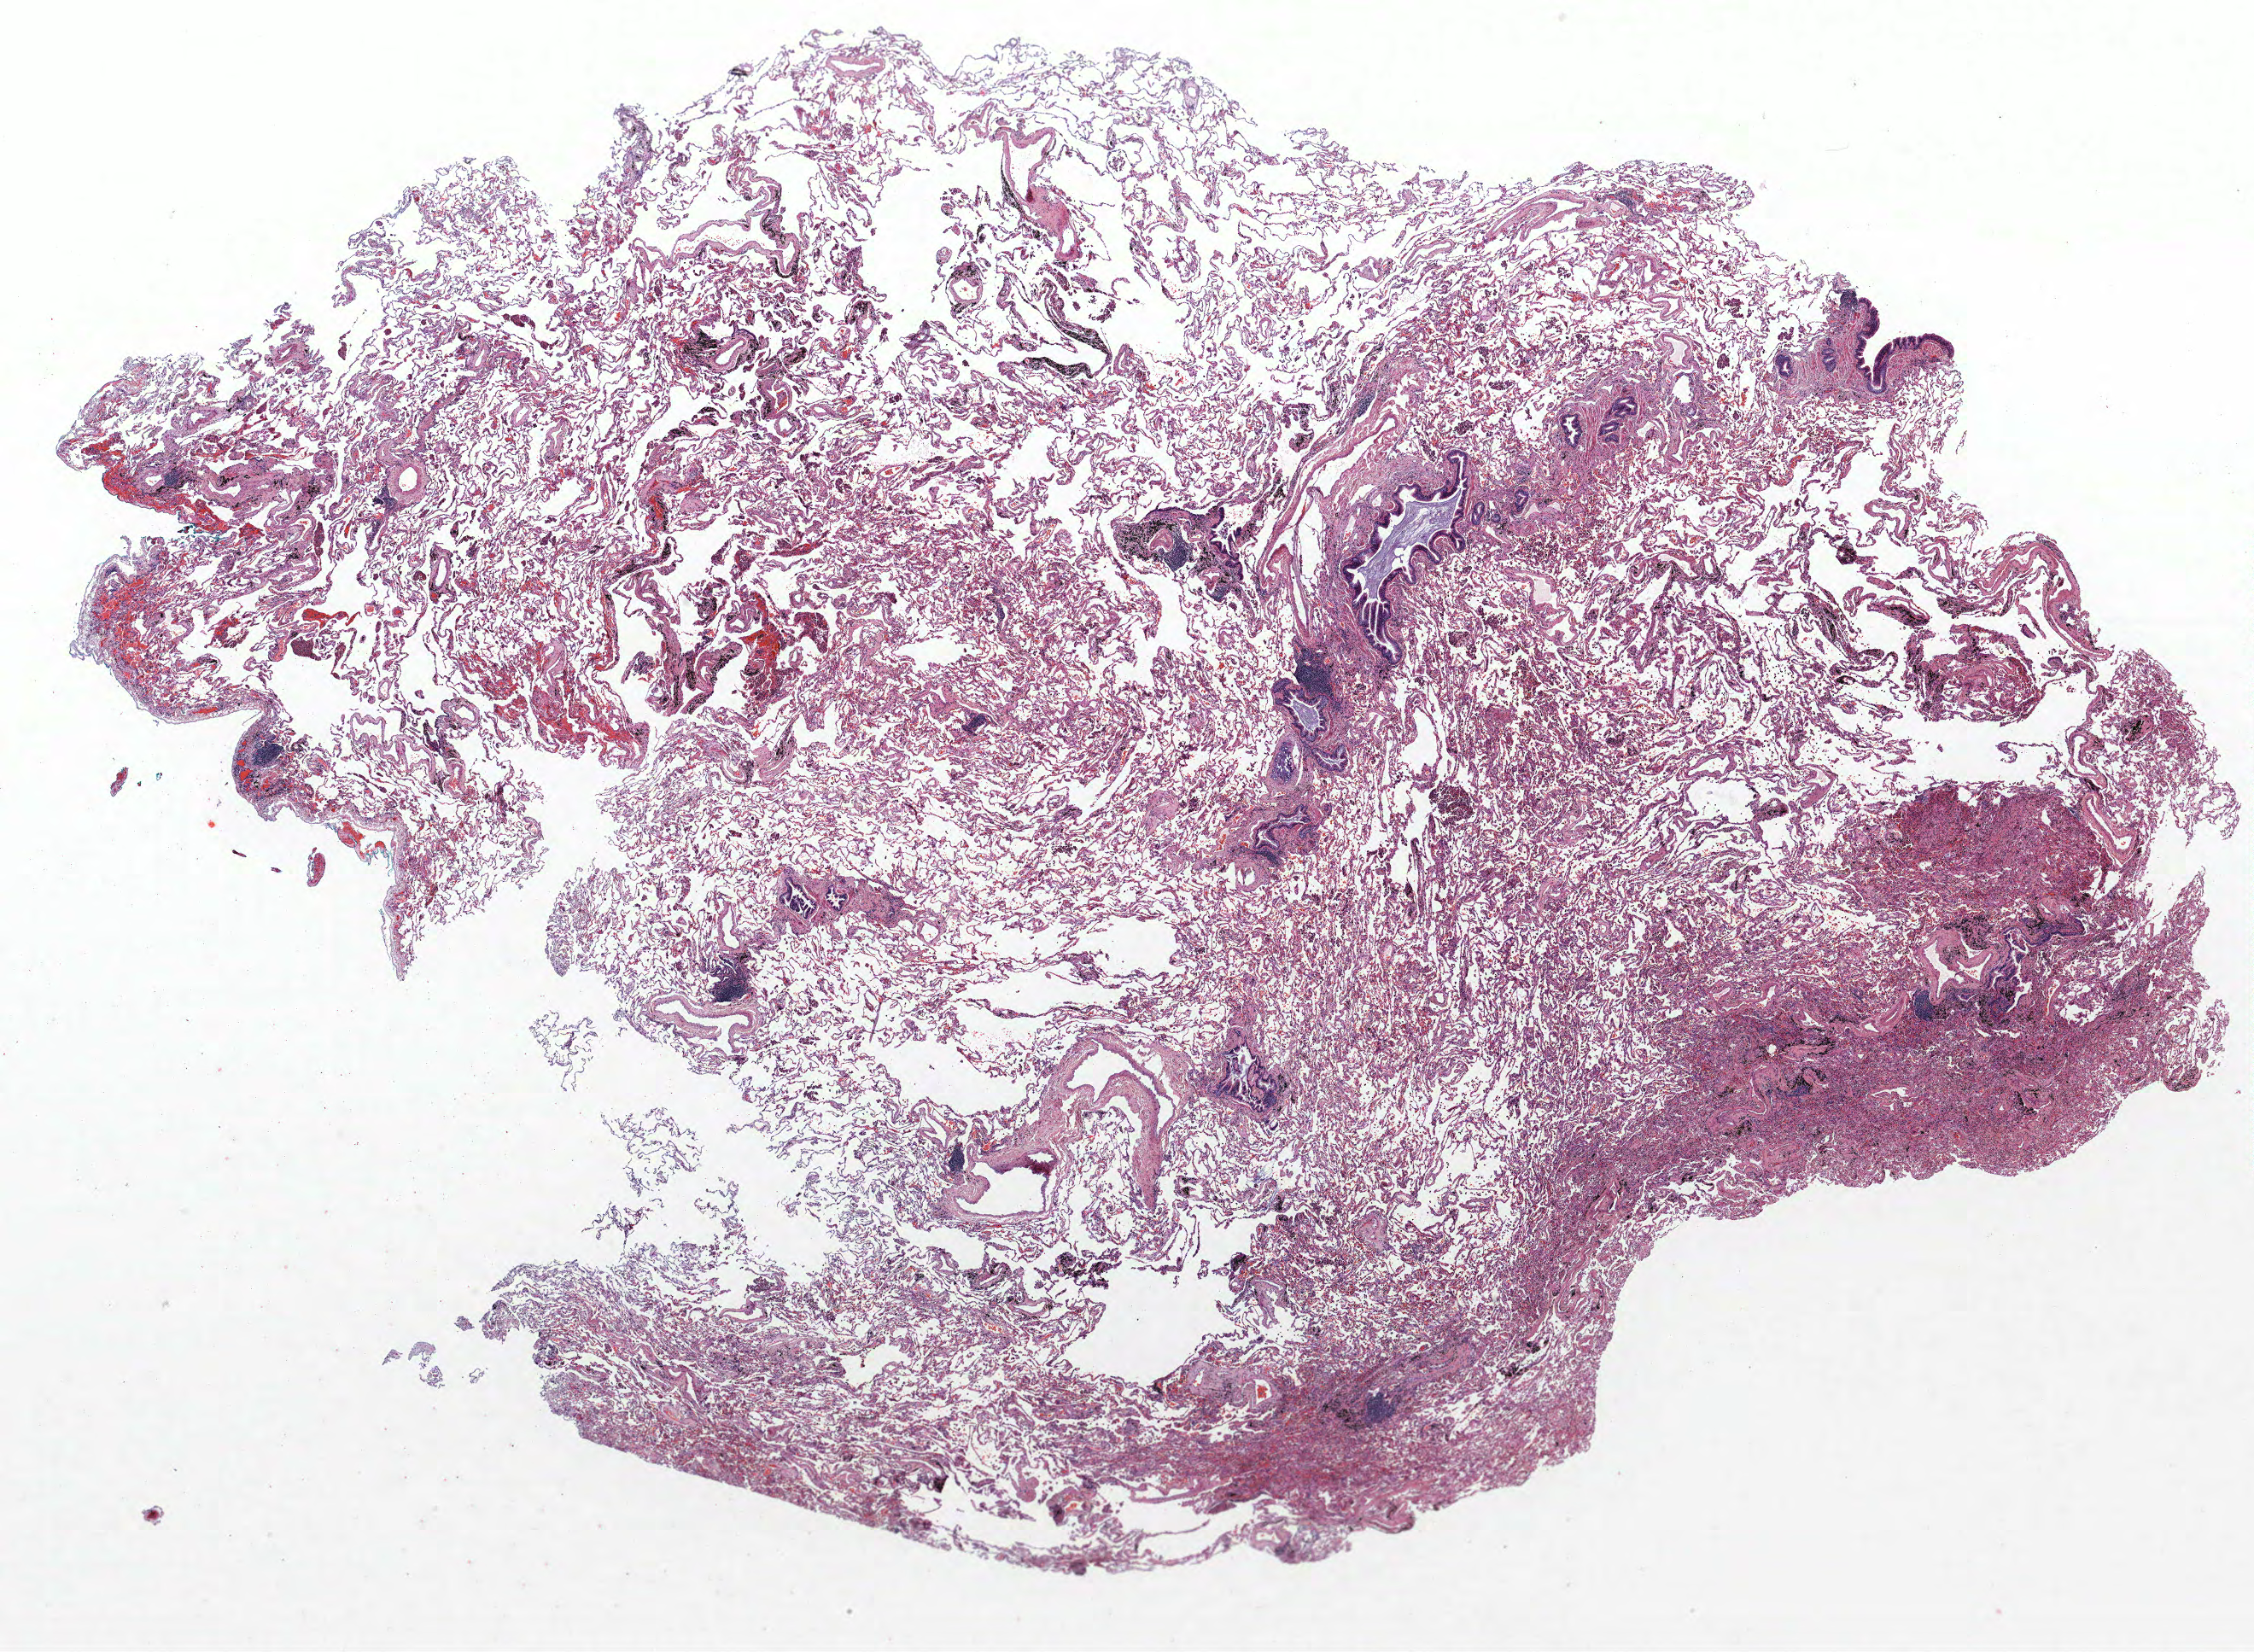
Whole-slide histology image, H&E — shown as a low-resolution overview of the whole scanned area (about 21.1 x 15.5 mm); FFPE section; lung tissue. Male patient, aged 69 at enrolment. Grade: poorly differentiated (G3).
Tumour size (pathology): 15 mm. Stage (AJCC 6th edition): IA. Primary tumour location (clinical record): right middle lobe. Participant's lung-cancer diagnosis: Squamous cell carcinoma, NOS.